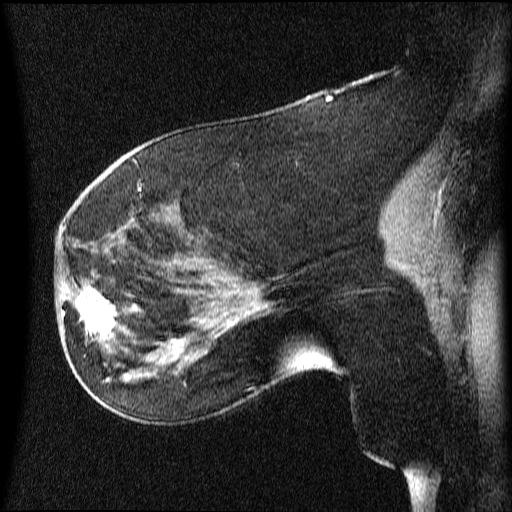
Breast MRI (dynamic contrast-enhanced), one sagittal slice; dynamic contrast-enhanced series, image 2 of 4 at this slice position (ordered by acquisition); 1.5 T; TE 4.2 ms, TR 9 ms; 512 × 512 image matrix, field of view 200 × 200 mm. Patient: female, 63 years.
Annotated regions visible in this slice (semi-automatically segmented with operator editing):
- analysis volume of interest (the breast-tissue region the enhancement analysis was run in; not a lesion): bounding box <66,272,131,353> (left, top, right, bottom; pixels)
- tumour enhancement mask (voxels above the 70 % enhancement threshold inside the analysis volume of interest): <69,286,124,339>